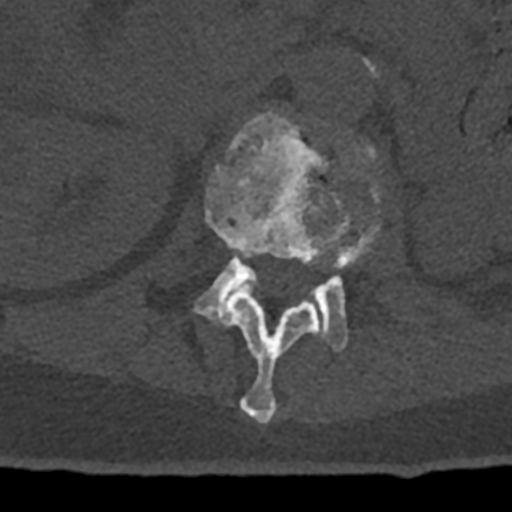
CT including the spine, one axial slice; position 409 of 797 along the scan axis; bone window (W 1800 / L 400 HU); 0.5 mm slice thickness; 512 × 512 image matrix, field of view 160 × 160 mm. Male patient, age 74 years. From the clinical record (not read from this slice): primary cancer: renal; vertebrae with lytic lesions (as recorded): T10, L1, L2, L3, L4, L5.
Structures marked on this image (semi-automatically segmented with operator editing):
- L1 vertebra: bounding box (x1, y1, x2, y2) in pixels: (204, 112, 351, 423)
- L2 vertebra: (195, 145, 379, 352)